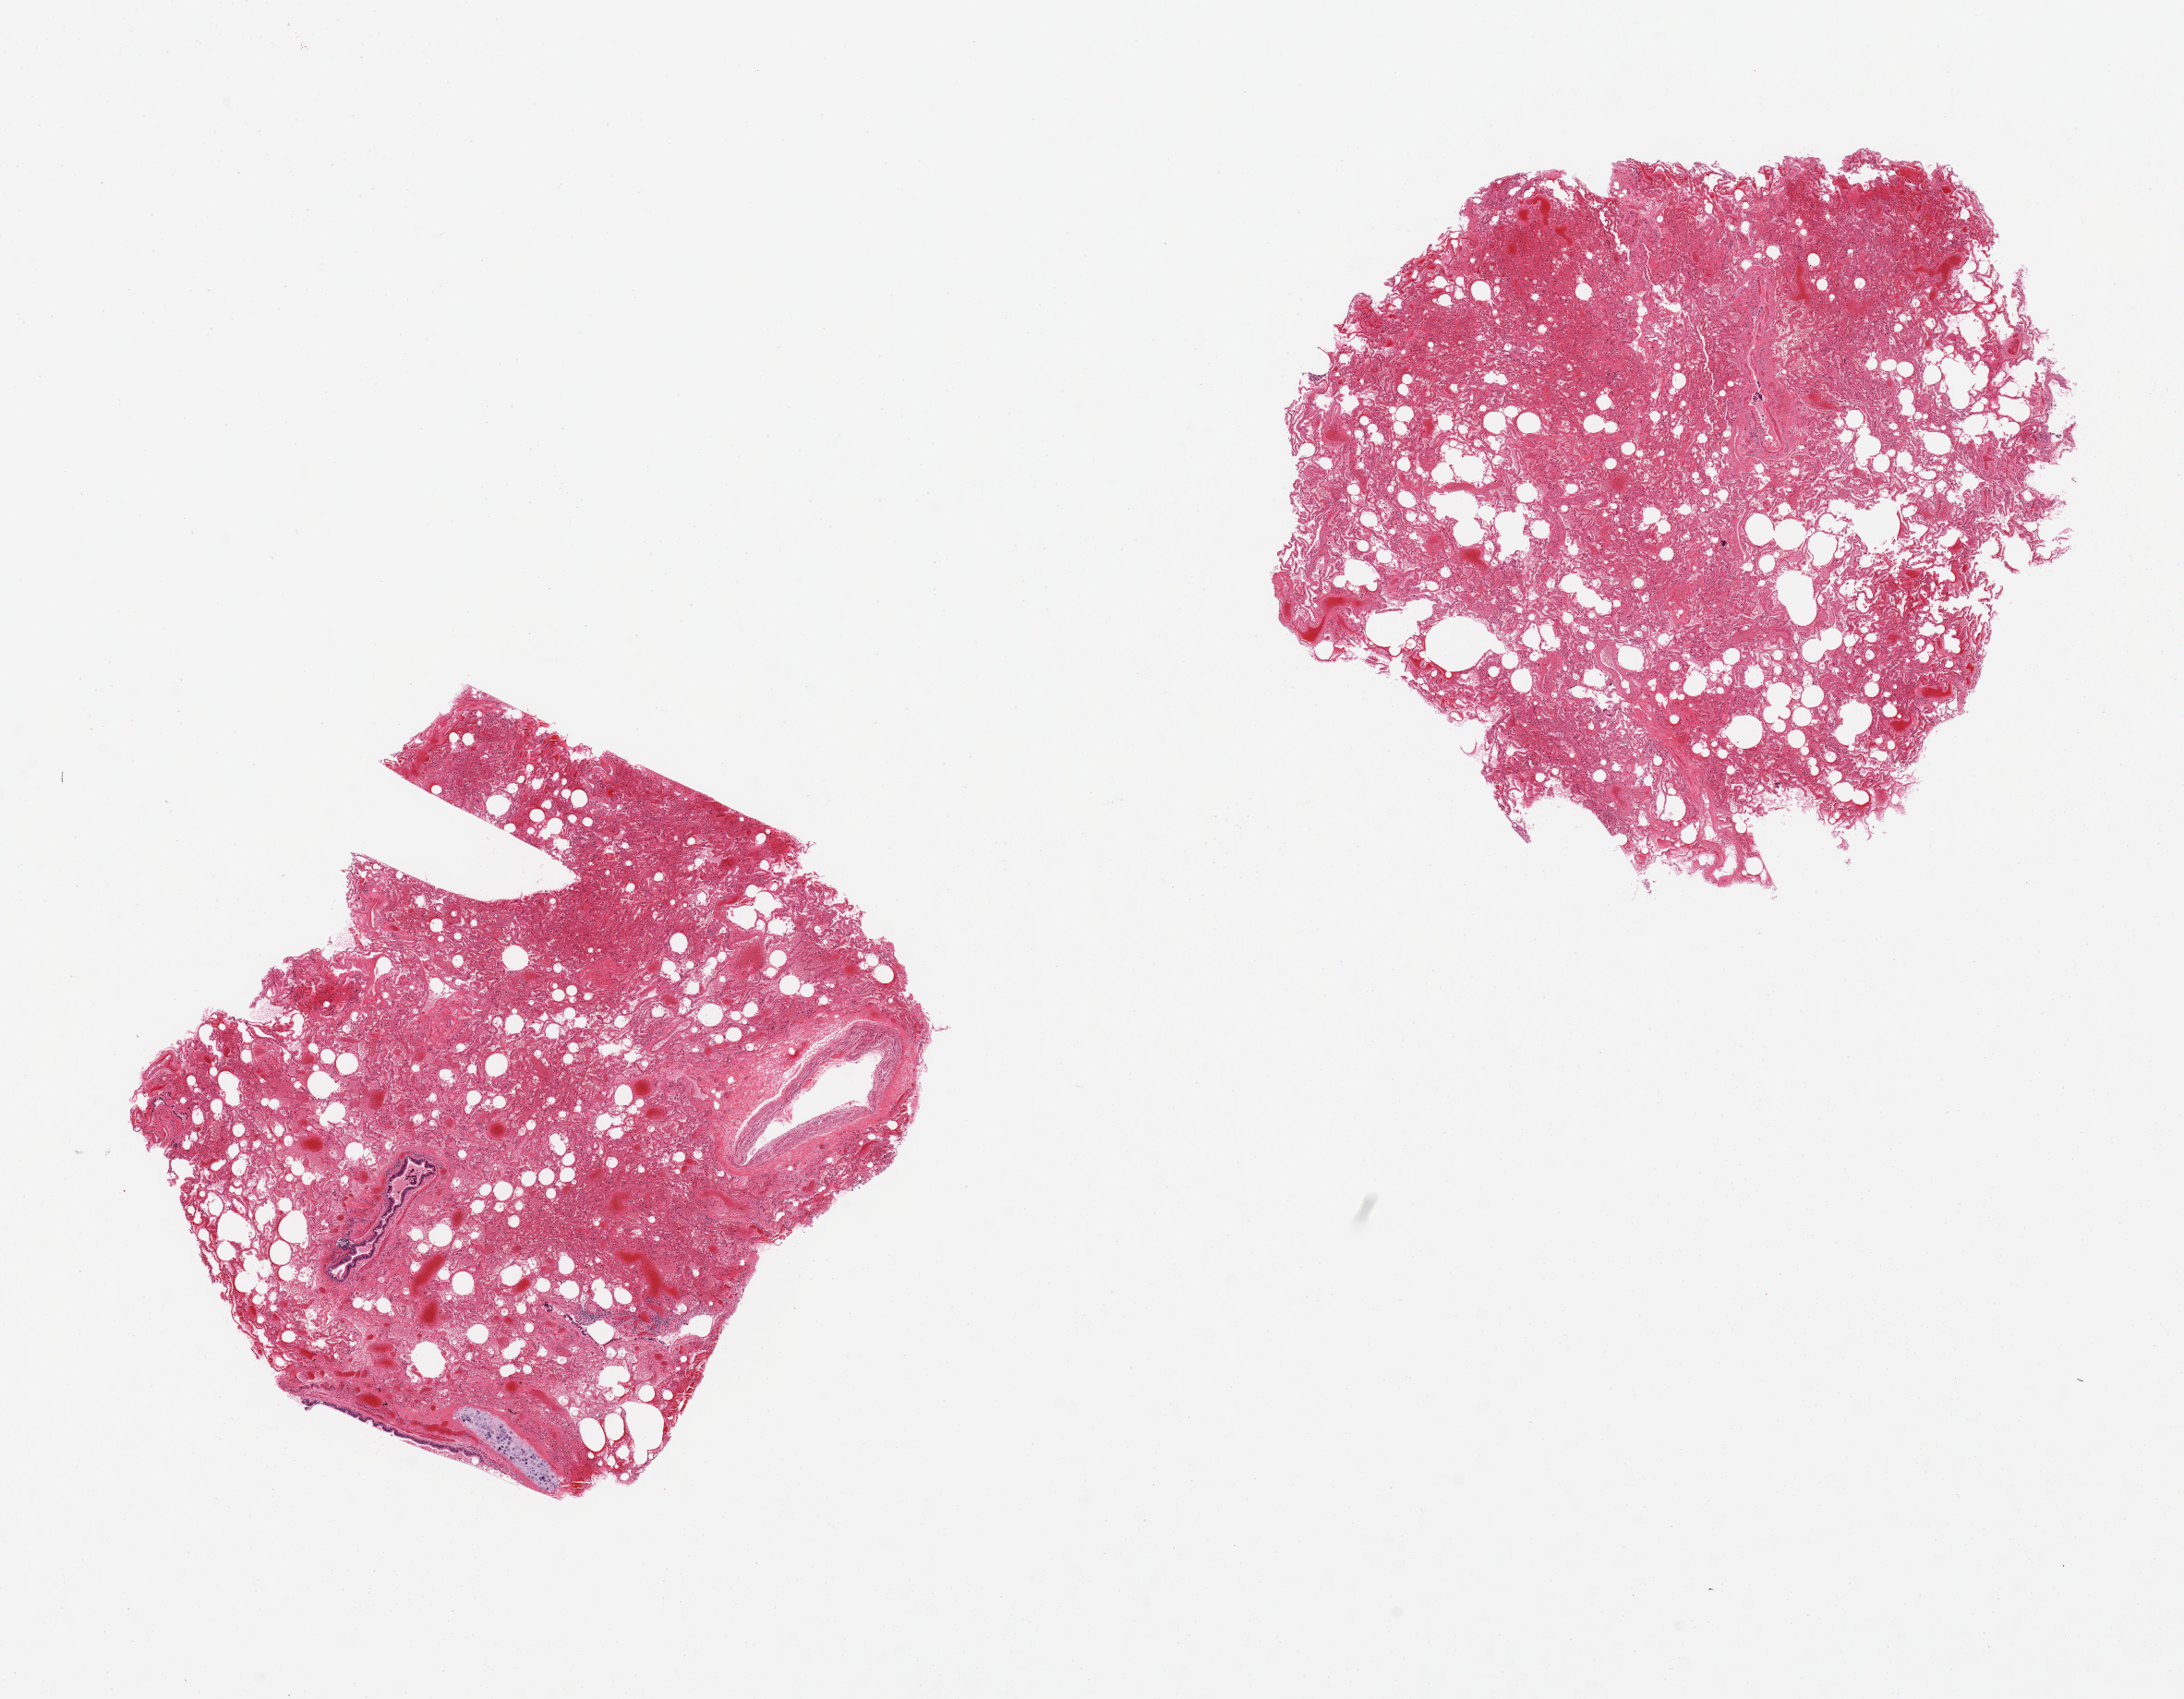
Hematoxylin and eosin (H&E) whole-slide image — whole scanned area (about 18.7 x 14.6 mm, from a 20x scan) shown as a low-resolution overview; PAXgene-fixed, paraffin-embedded tissue; sampled site (target tissue): lung; donor tissue sample. Male donor.
Pathologist's review note for this sample: 2 pieces, one piece includes large vessel and focus of cartilage, congestion.